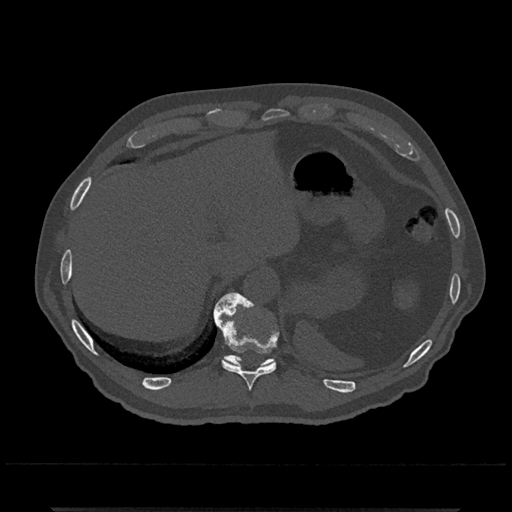
CT including the spine, one axial slice. Position 536 of 797 along the scan axis. 120 kVp. Bone window (W 1800 / L 400 HU). 0.5 mm slice thickness. 512 × 512 image matrix. Patient: male, 67 years. Case-level facts recorded for this patient, not image findings: primary cancer: prostate.
Structures marked on this image (semi-automatically segmented with operator editing):
- T10 vertebra: bounding box (x1, y1, x2, y2) in pixels: (214, 292, 277, 391)
- T11 vertebra: (214, 294, 276, 367)